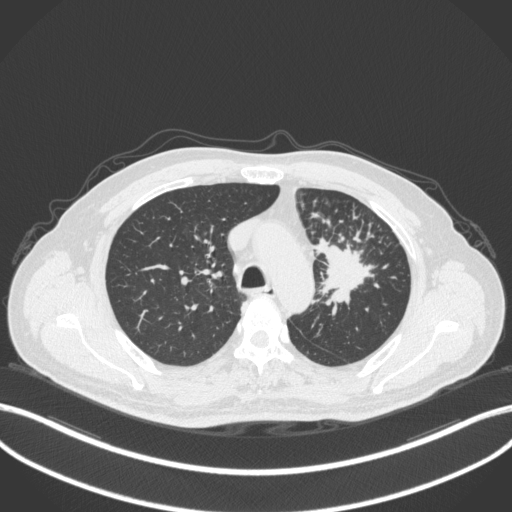
Chest CT, one axial slice; position 260 of 386 along the scan axis; reconstruction kernel B31f; 120 kVp; lung window (W 1500 / L -600 HU); 1 mm slice thickness; 512 × 512 image matrix. Male patient, age 69 years. From the clinical record (not read from this slice): clinical TNM (as recorded): T2a N2 M0; histopathological grade: G2-3.
Annotated regions visible in this slice (bounding box drawn by a radiologist):
- lung tumour (recorded histology: adenocarcinoma): bounding box [x1, y1, x2, y2] px = [314, 235, 381, 309]